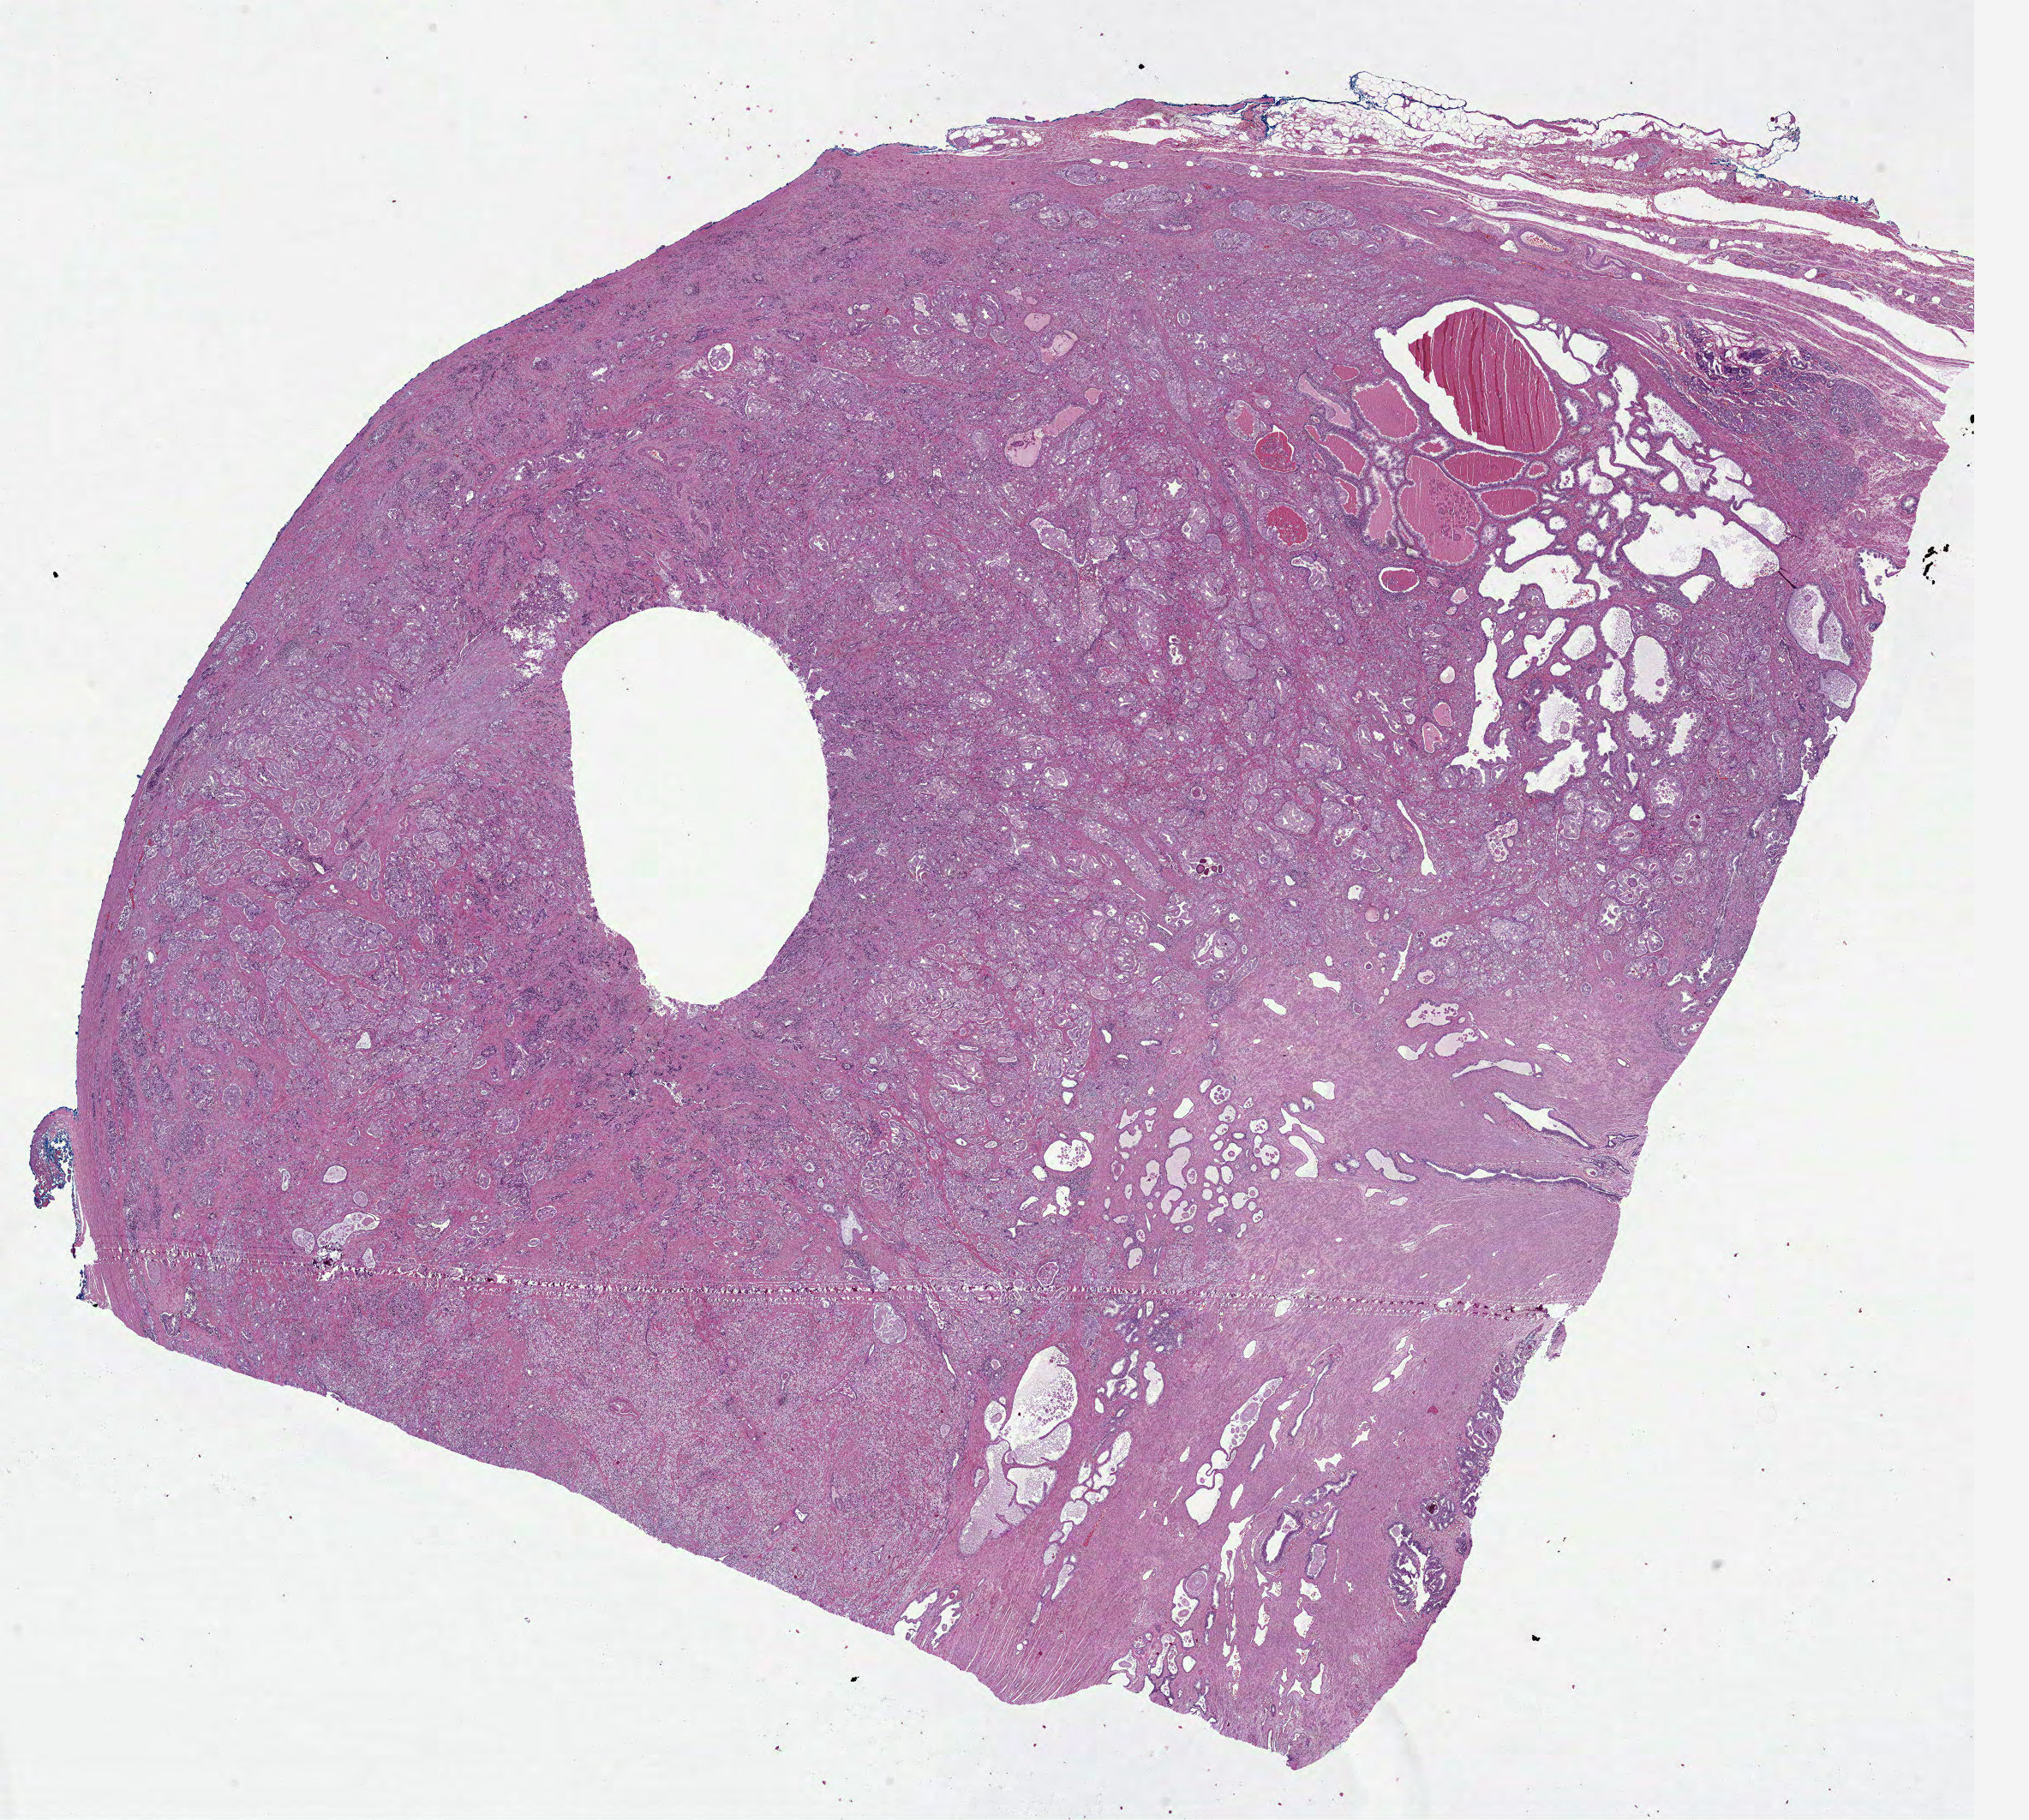
Digitized Hematoxylin and eosin (H&E) stained tissue section (whole slide), low-resolution overview of the scanned area, about 19.1 x 17.1 mm (acquisition: 40x scan). Formalin-fixed paraffin-embedded (FFPE) diagnostic section. Sample: primary tumour, prostate. Male patient; age at initial diagnosis 67 years. Gleason score: 9 (4+5).
• laterality: bilateral
• lymph nodes positive (case pathology): 0 of 2 examined
• diagnosis: Adenocarcinoma, NOS (prostate gland)